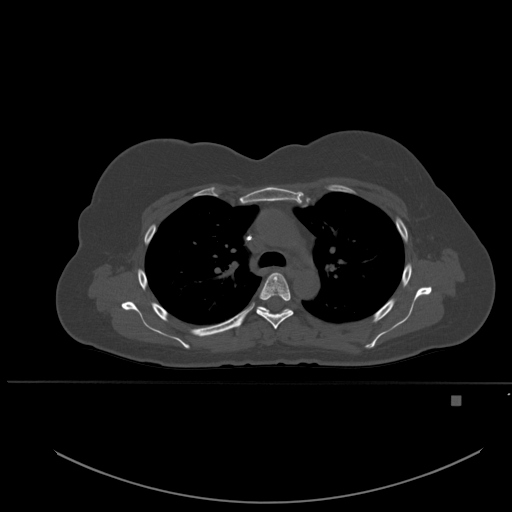
CT including the spine, one axial slice; slice 377 of 651 in the series (ordered by position); bone window (W 1800 / L 400 HU); 512 × 512 image matrix, field of view 443 × 443 mm. Female patient, age 49 years. From the clinical record (not read from this slice): primary cancer: breast; vertebrae with lytic lesions (as recorded): L3, T12, L4.
Annotated regions visible in this slice (semi-automatic segmentation, software-assisted and operator-edited):
- T4 vertebra: bounding box <256,272,294,329> (left, top, right, bottom; pixels)
- T5 vertebra: <242,306,292,322>